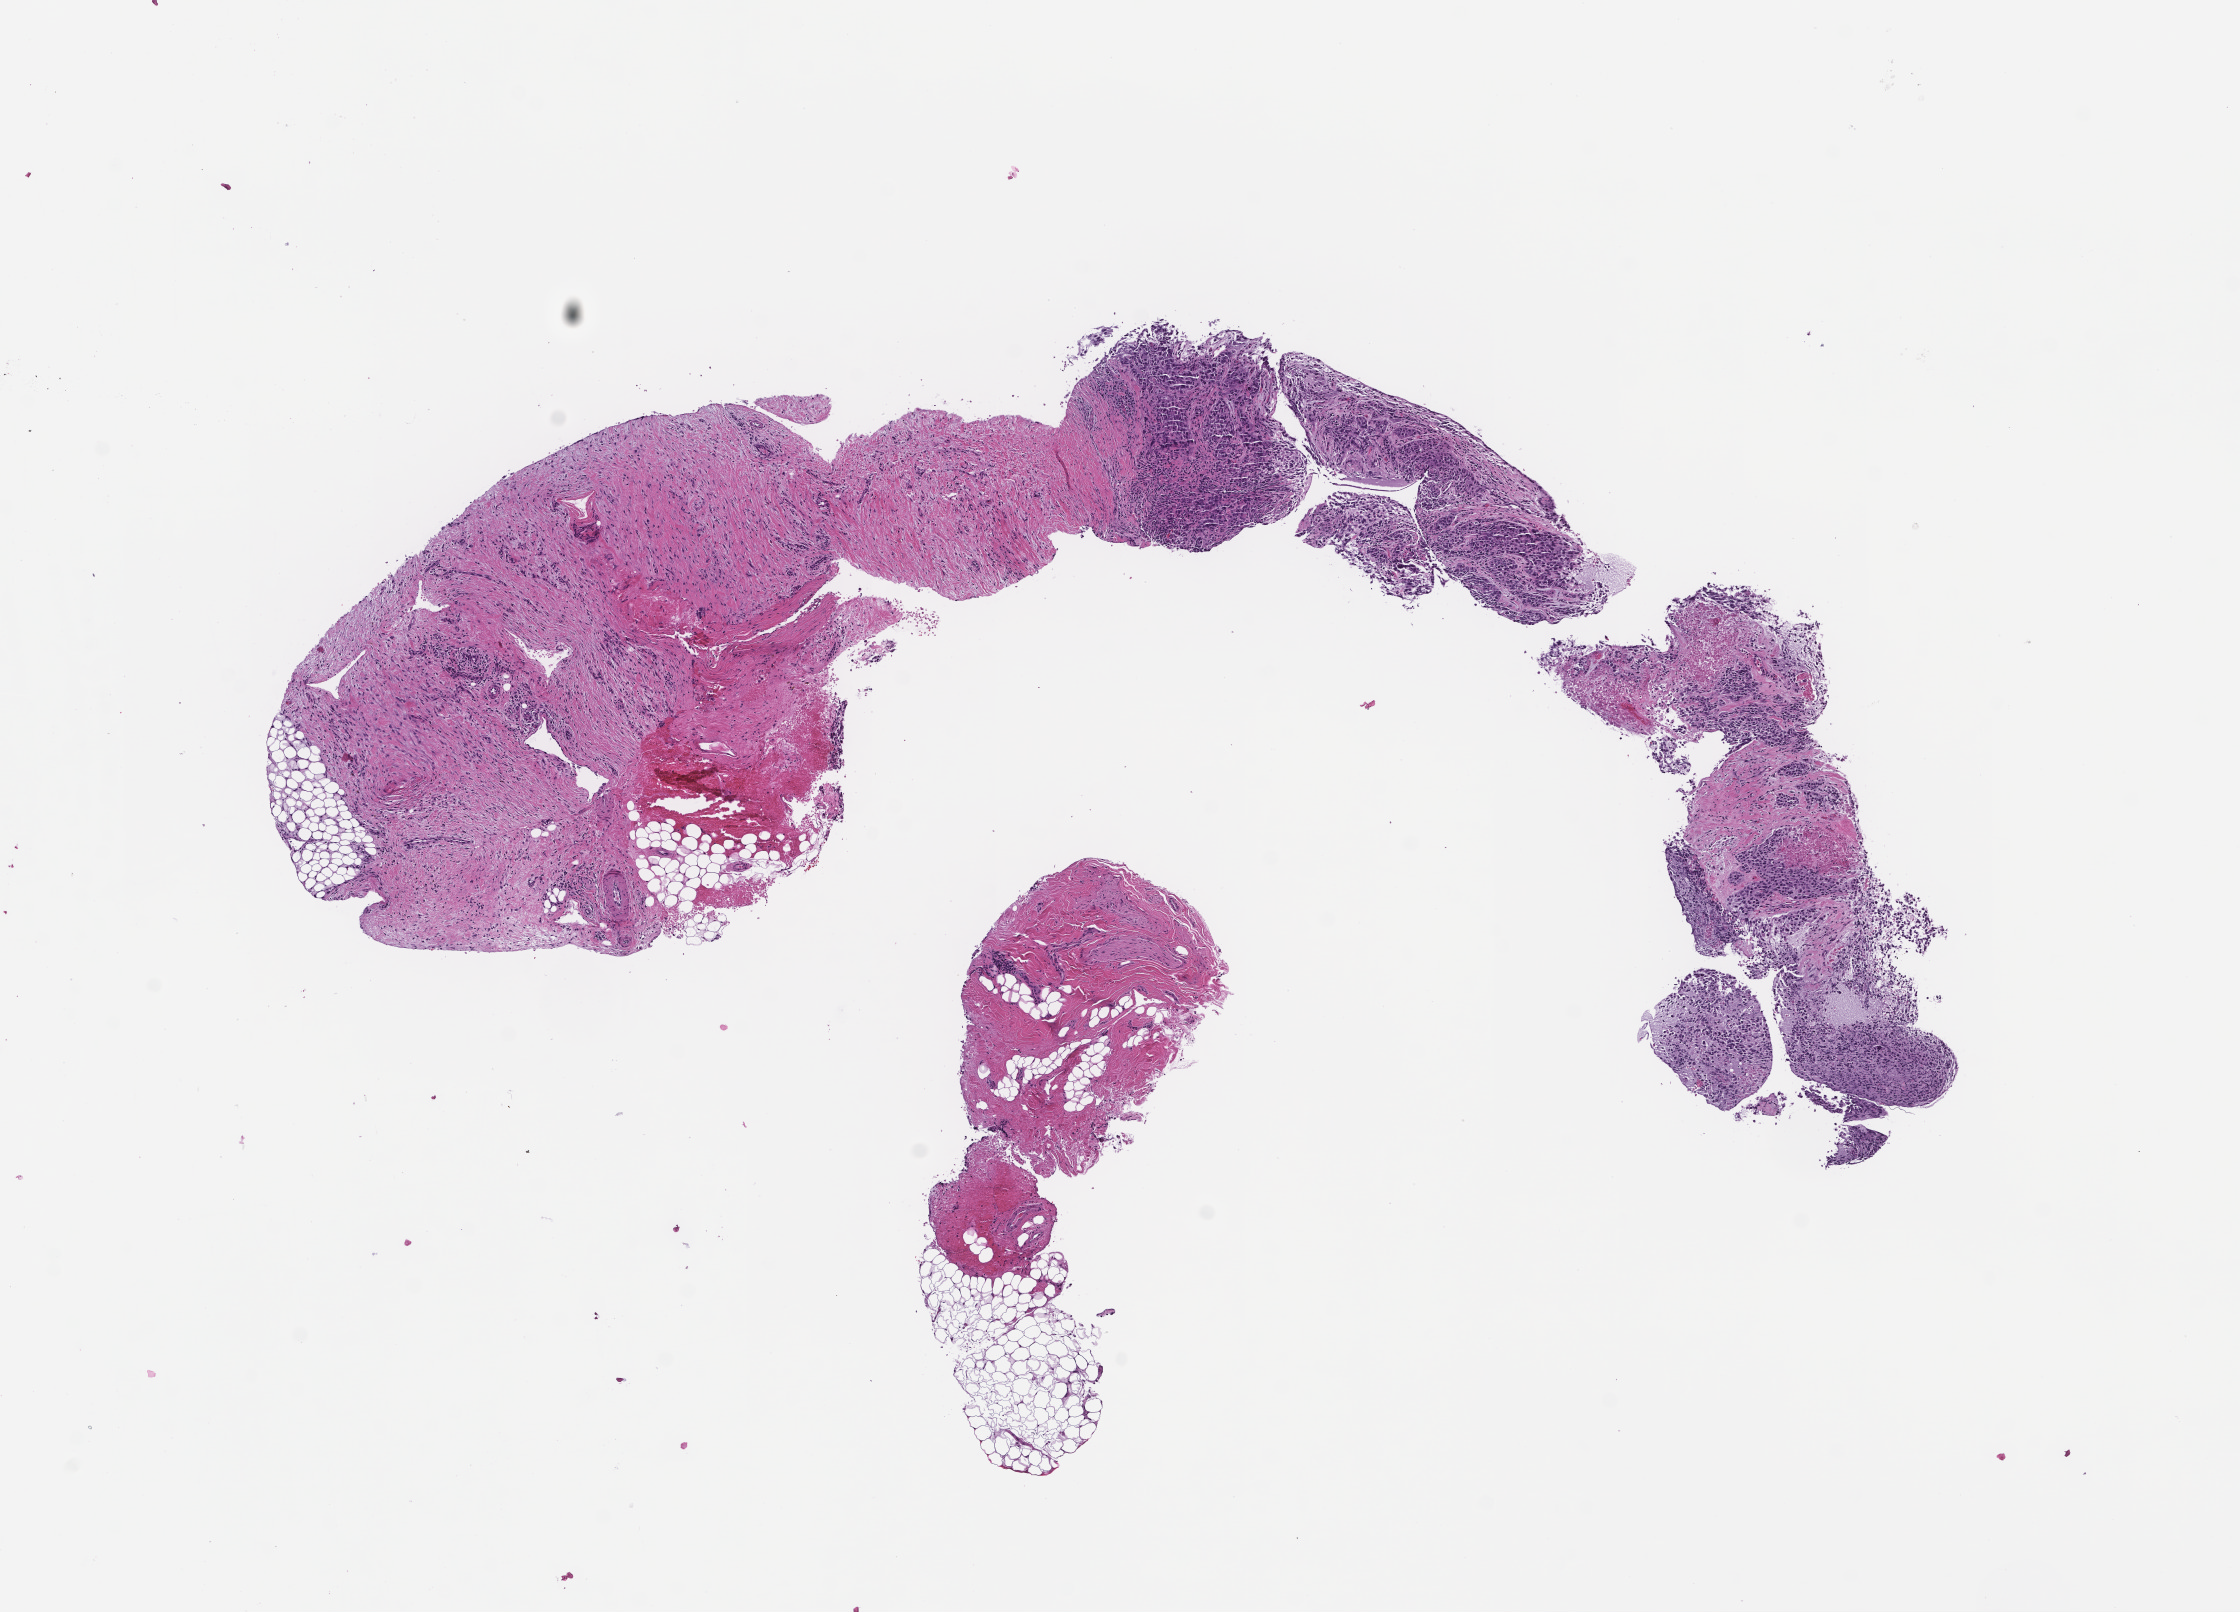
Whole-slide image, hematoxylin and eosin (H&E) stain, a low-resolution overview of the entire scanned area, about 9.0 x 6.5 mm; FFPE section. Patient: male.
This section: metastatic tumor tissue. Patient diagnosis (primary): Small Cell Lung Carcinoma.